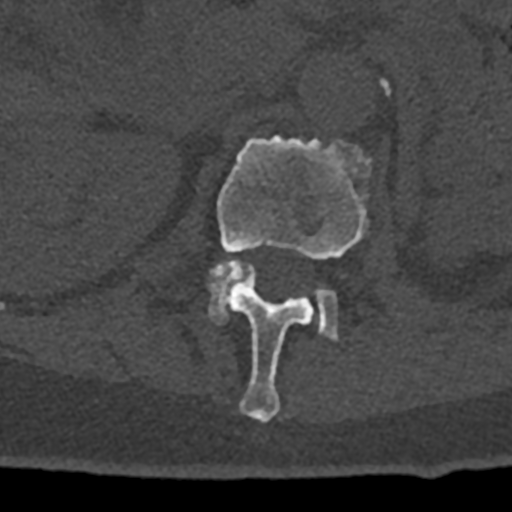
CT including the spine, one axial slice. Position 421 of 797 along the scan axis. Reconstruction kernel Br40s/3. Bone window (W 1800 / L 400 HU). 512 × 512 image matrix, field of view 160 × 160 mm. Patient: male, 74 years. From the clinical record (not read from this slice): primary cancer: renal; vertebrae with lytic lesions (as recorded): T10, L1, L2, L3, L4, L5.
Annotated regions visible in this slice (semi-automatically segmented with operator editing):
- L1 vertebra: bounding box [x1, y1, x2, y2] px = [217, 136, 370, 422]
- L2 vertebra: [208, 260, 338, 340]